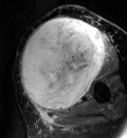
MRI of an extremity soft-tissue mass, one axial slice. Slice 40 of 87 in the series (ordered by position). T2-weighted fat-saturated. MR volume resampled by the dataset authors to the PET/CT grid (not the native acquisition matrix). 3.27 mm slice thickness. 127 × 138 image matrix. Female patient. From the clinical record (not read from this slice): histological type: pleiomorphic leiomyosarcoma; grade: high; site of the primary tumour: left biceps.
Annotated regions visible in this slice (expert contour drawn on MRI and transferred to this co-registered scan by the dataset authors):
- gross tumour volume including surrounding oedema: box from (x=20, y=18) to (x=108, y=113) px
- gross tumour volume (mass): (x=20, y=18)–(x=107, y=111)